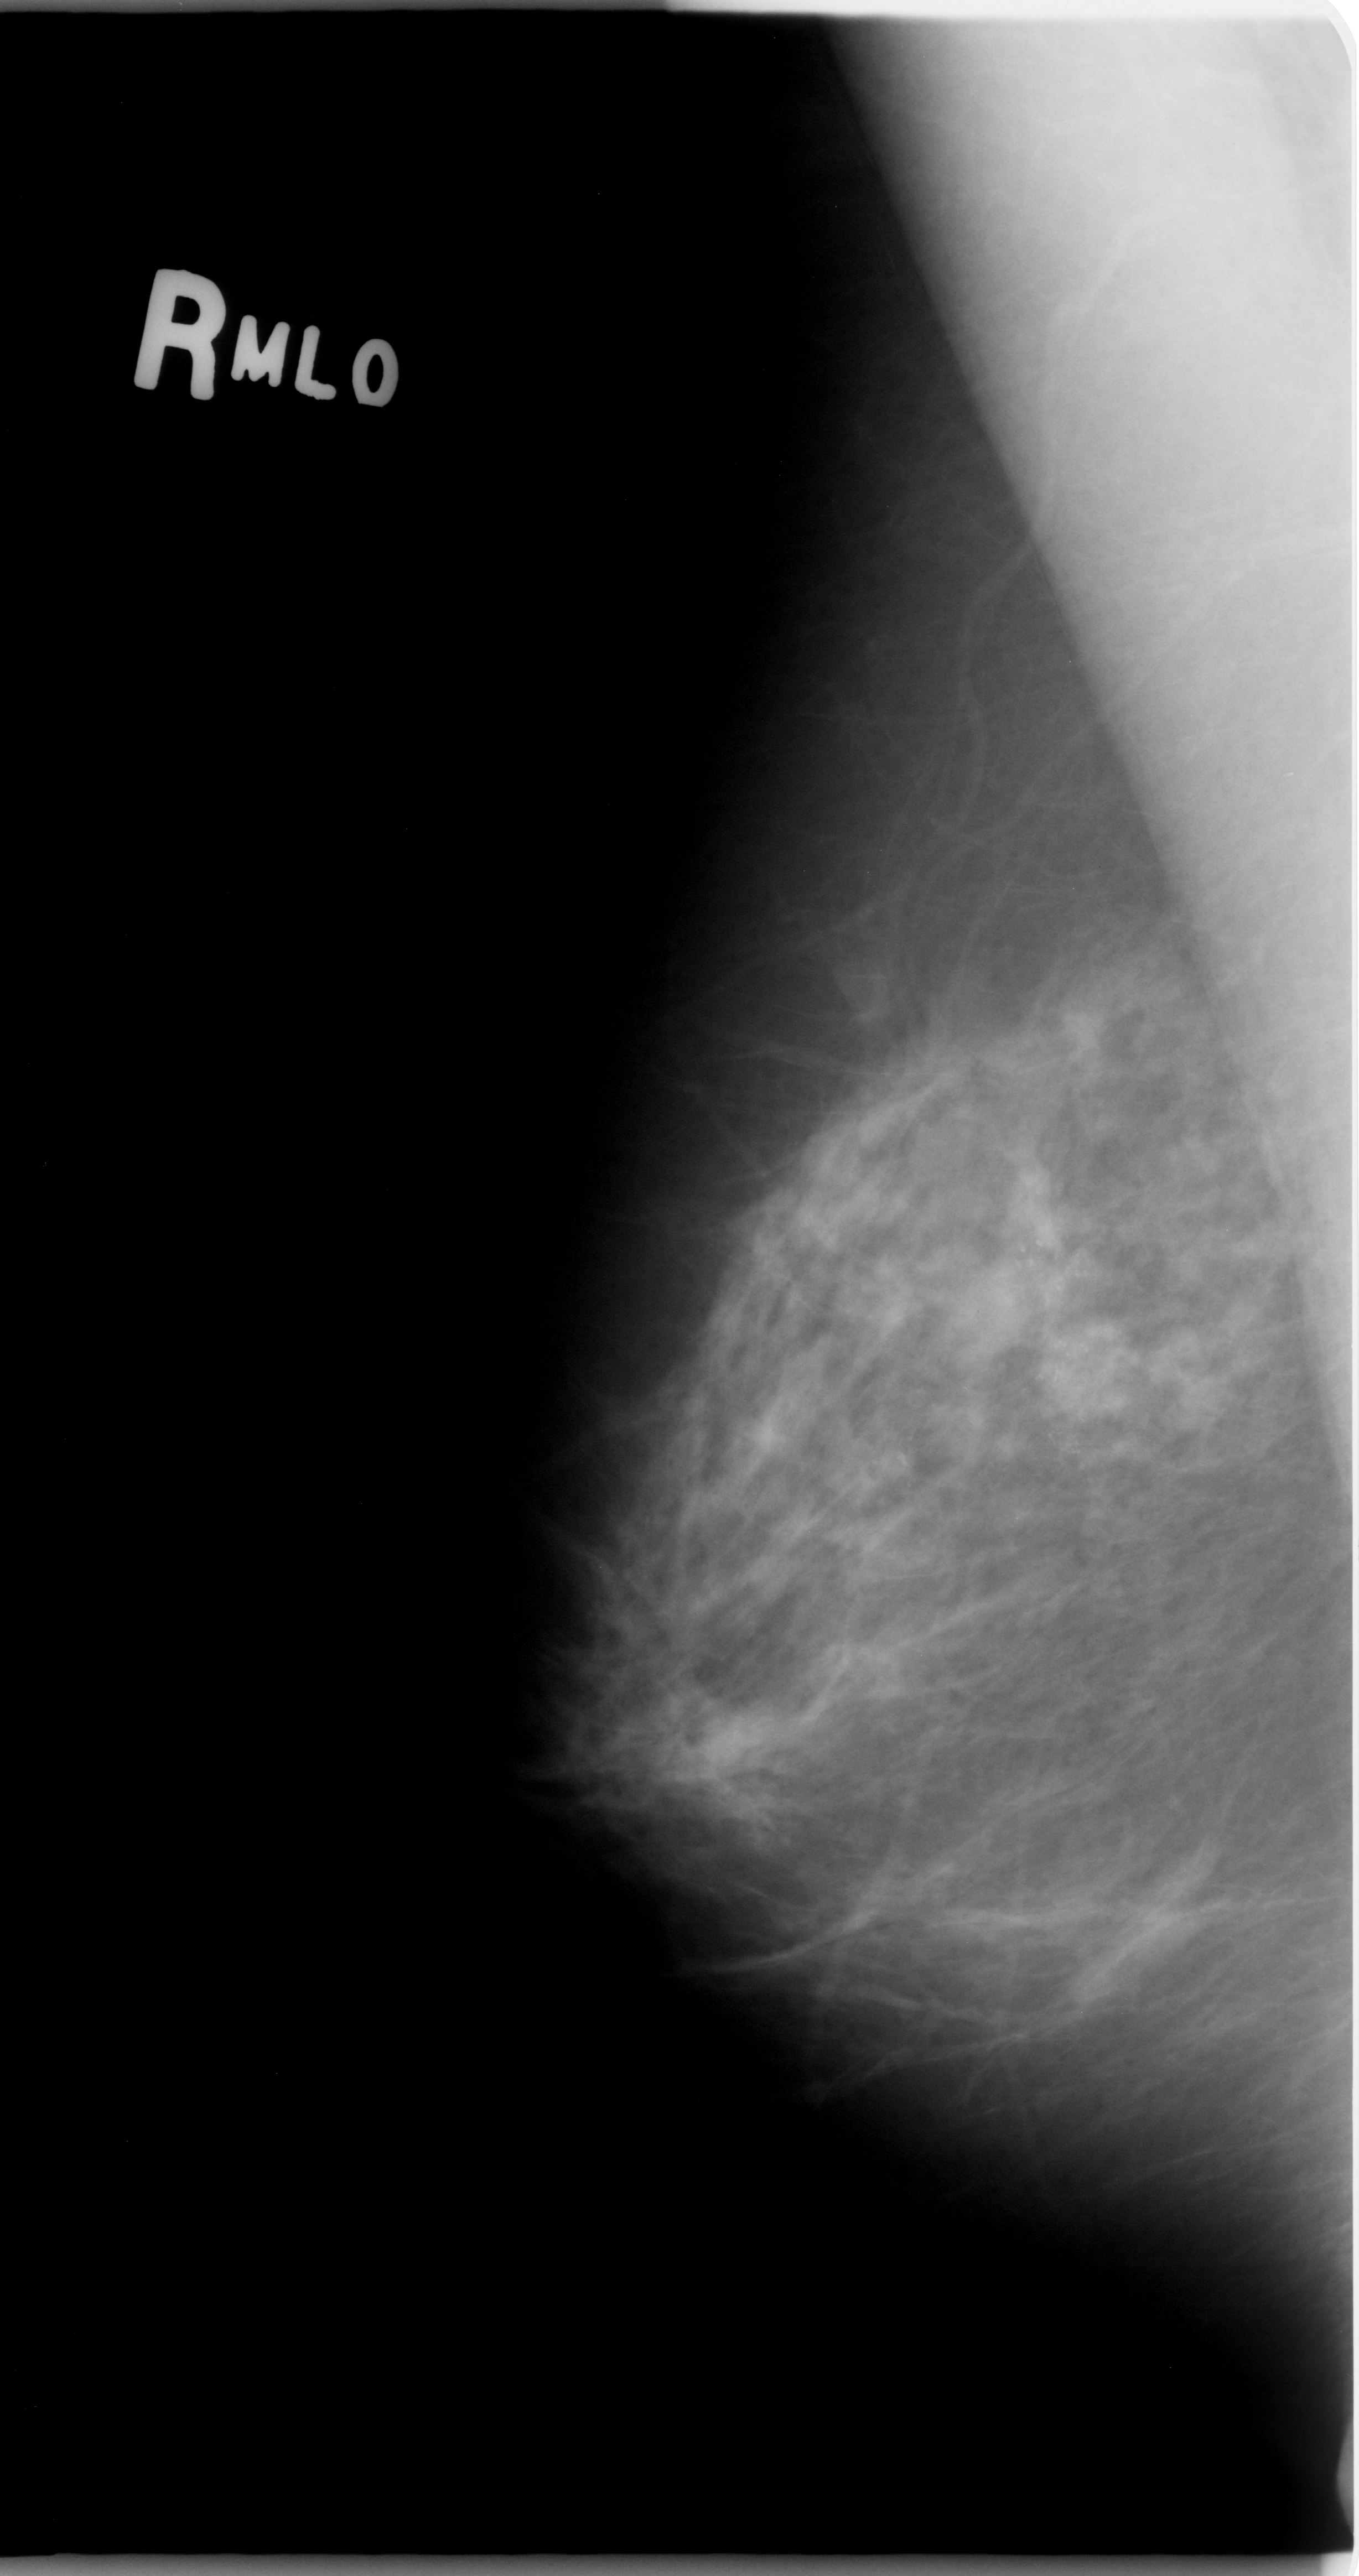
Mammogram (digitized film); right breast; MLO view; BI-RADS breast density category 2 (scale 1–4).
Calcifications, morphology pleomorphic, distribution clustered; BI-RADS assessment category 5; subtlety rating 5 on a 1 (subtle) to 5 (obvious) scale; pathology result (as recorded, not read from the image): malignant.